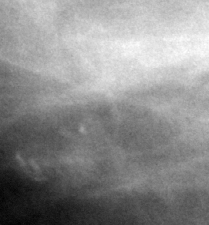
Crop from a digitized film mammogram around one marked abnormality; right breast; MLO view; BI-RADS breast density category 2 (scale 1–4).
Marked abnormality: calcifications, morphology round and regular / pleomorphic, distribution clustered; BI-RADS assessment category 4; pathology result (as recorded, not read from the image): benign.